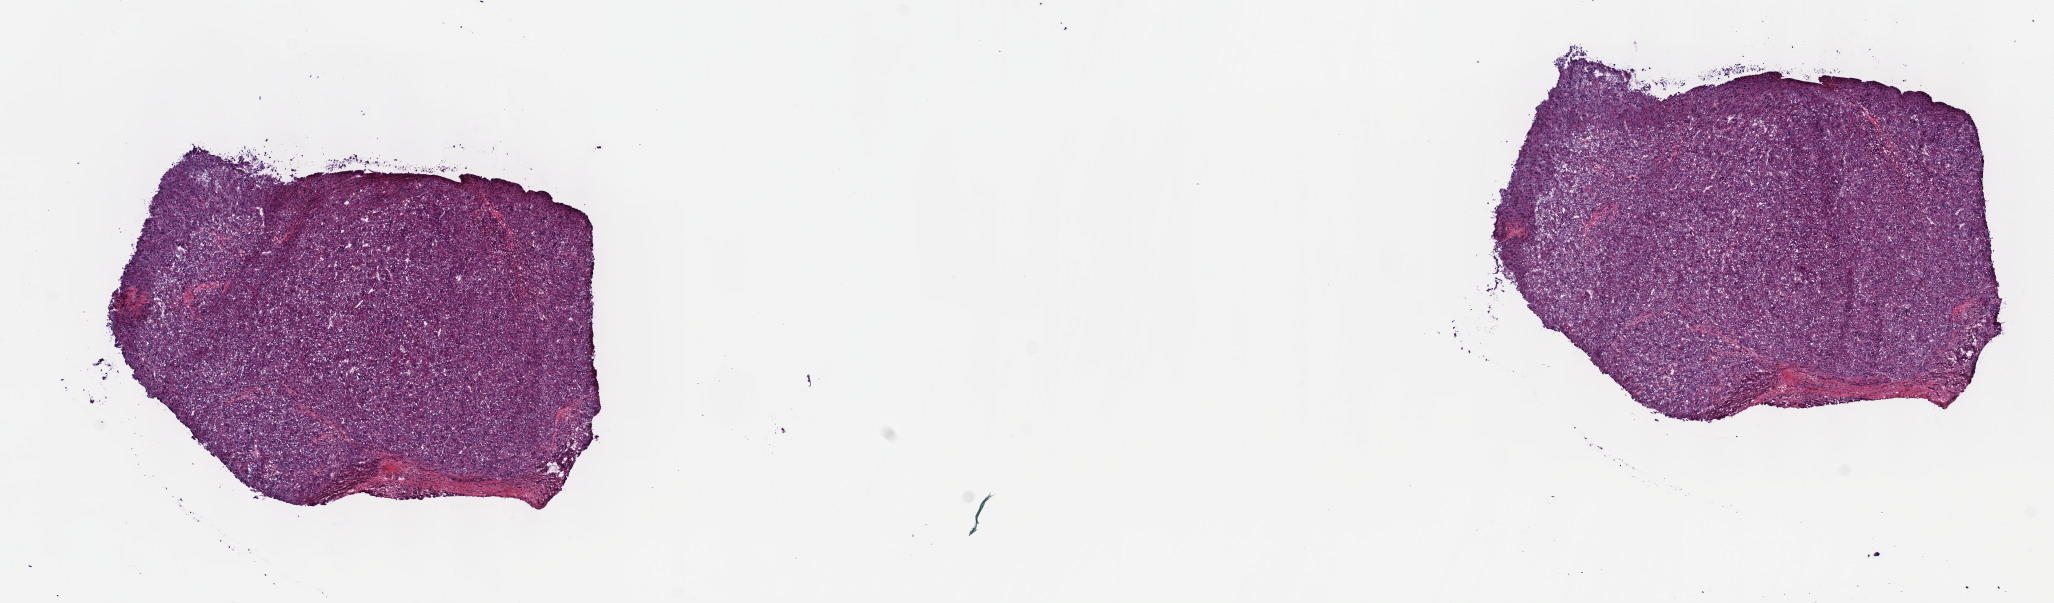
Hematoxylin and eosin (H&E) stained whole-slide image — a low-resolution overview of the entire scanned area, about 16.6 x 4.9 mm (acquisition: 40x scan), frozen section, liver, primary tumour sample. Male, age 68 years at initial diagnosis. Histologic grade: G3 (poorly differentiated). Pathologist review of this section (percent, as recorded): tumour cells 90%, tumour nuclei 95%, normal cells 0%, stromal cells 8%, necrosis 2%. Inflammatory infiltration, as recorded: lymphocyte infiltration 3%, monocyte infiltration 1%, neutrophil infiltration 1%.
AJCC pathologic stage: IIIA (7th edition). Histologic diagnosis: Hepatocellular carcinoma, NOS.